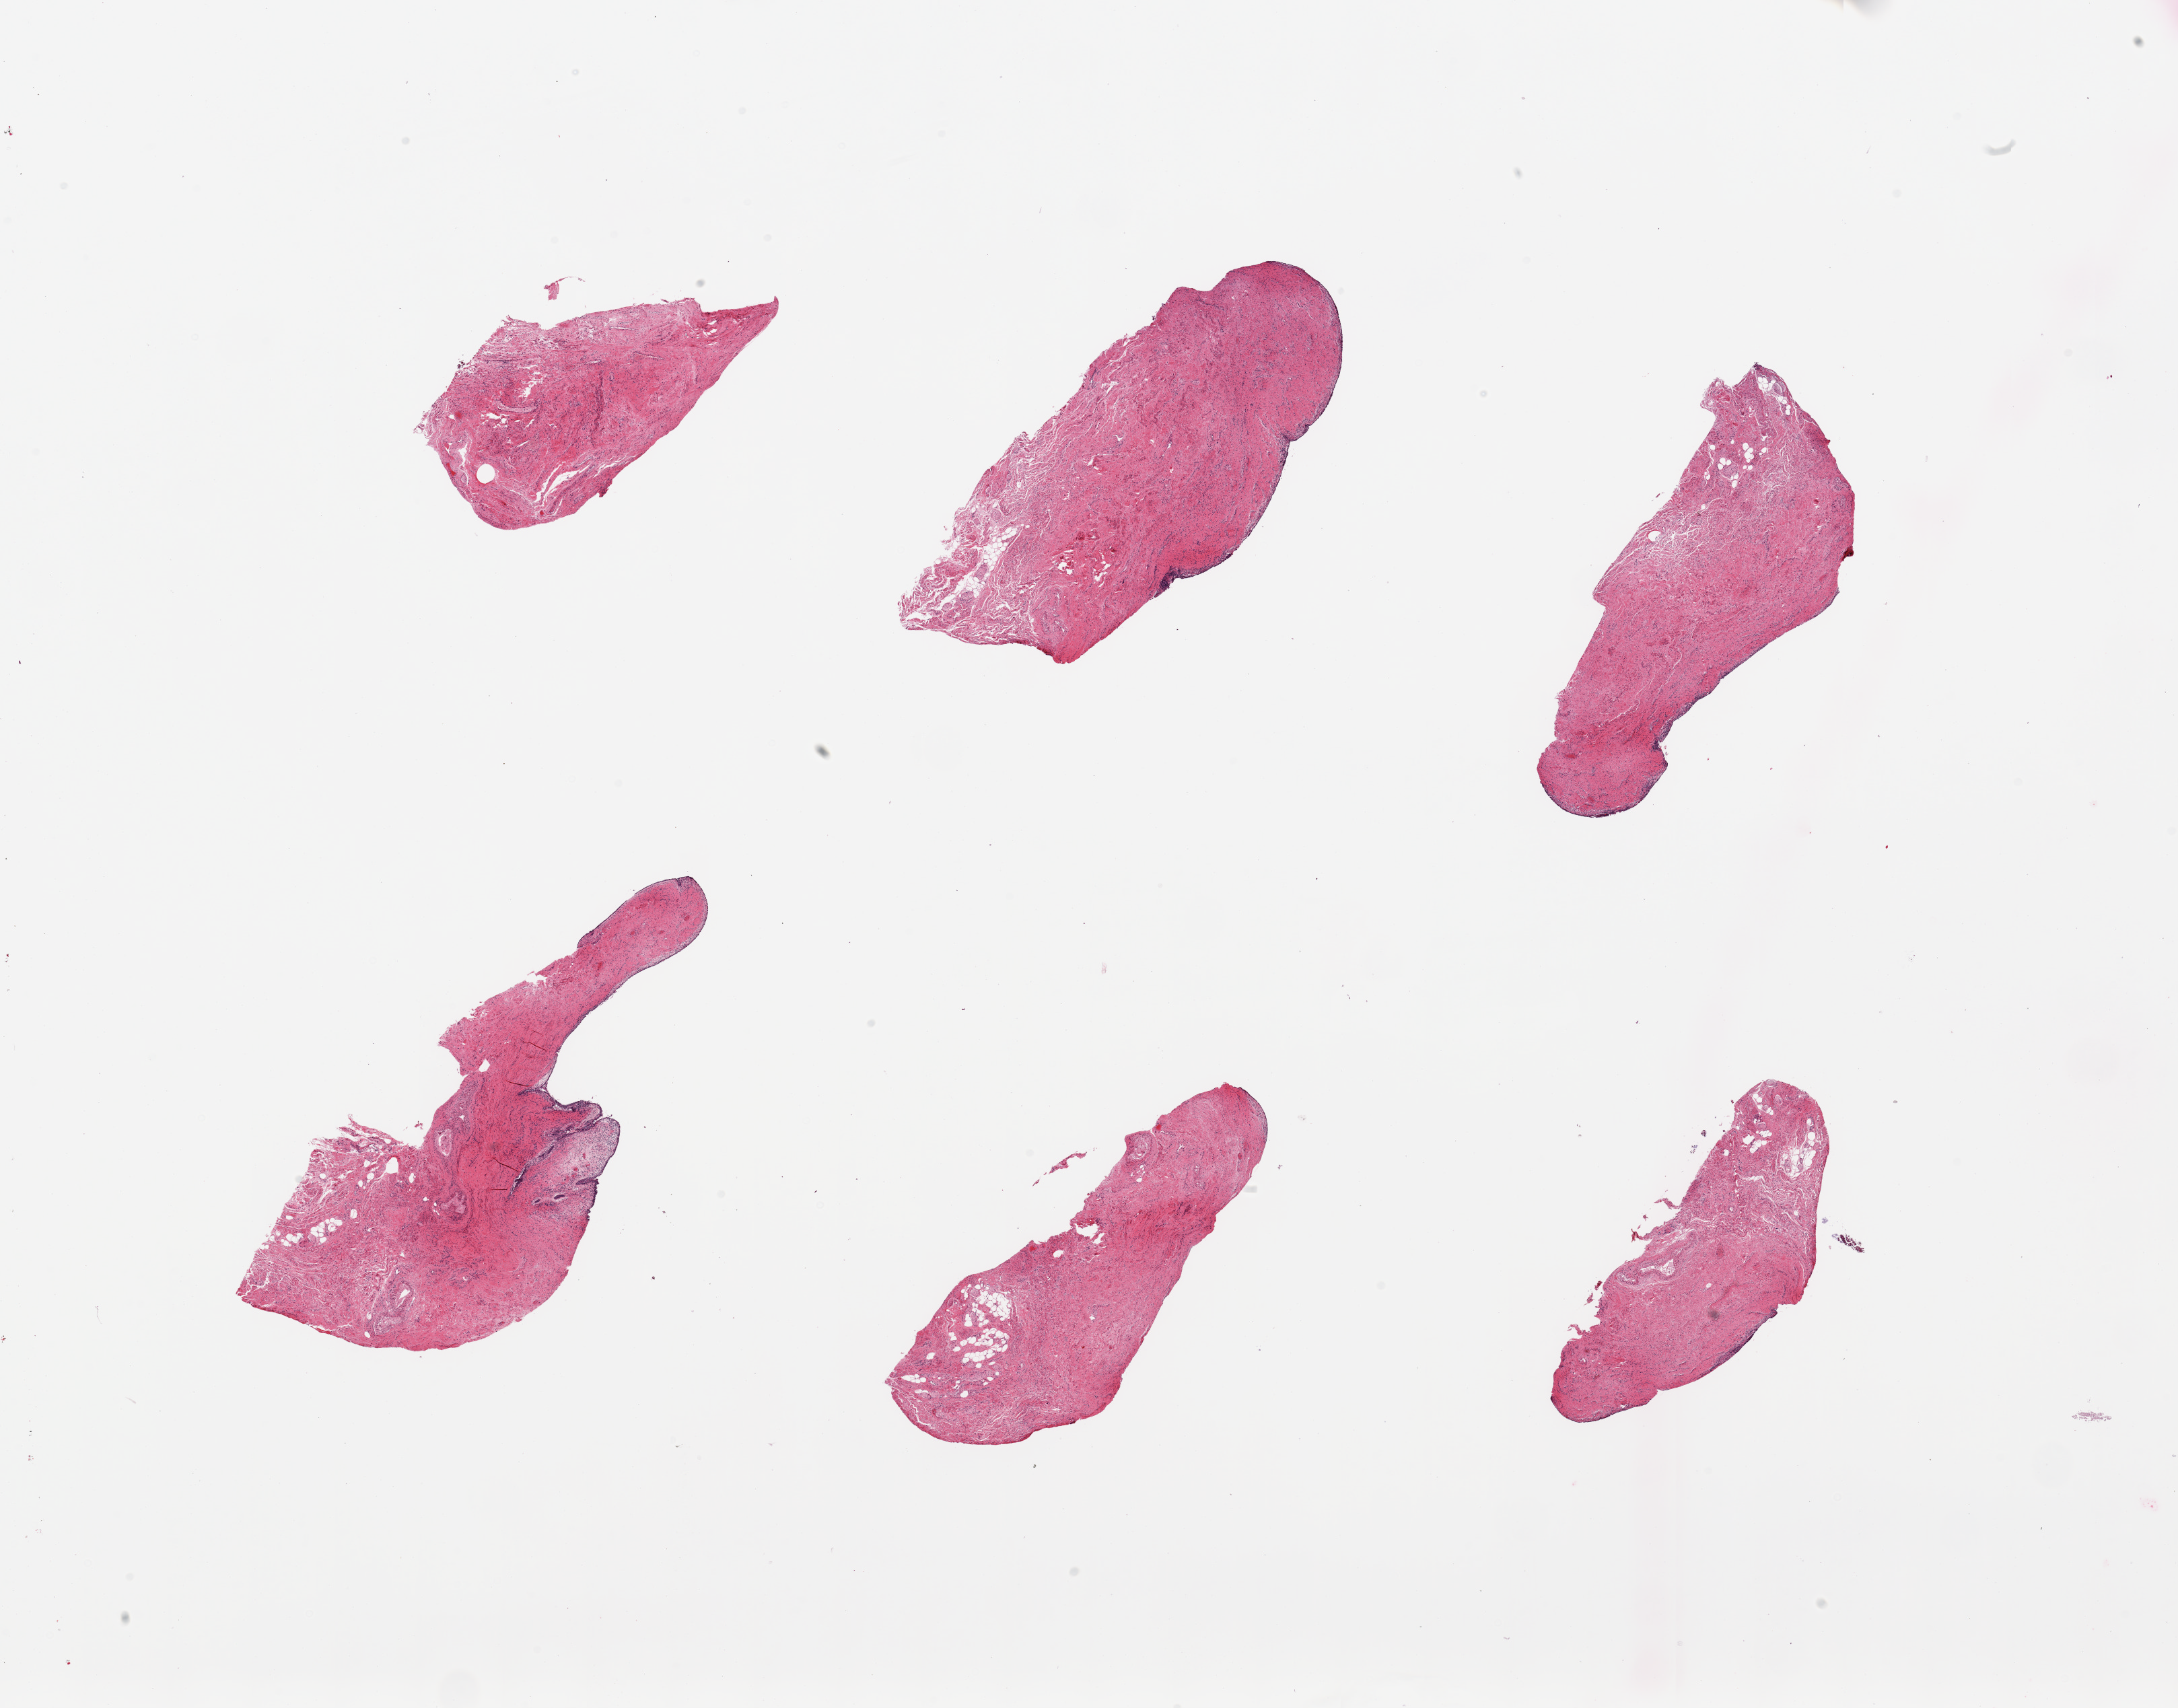
Haematoxylin and eosin whole-slide image, whole scanned area (about 25.6 x 20.1 mm) shown as a low-resolution overview; PAXgene-fixed, paraffin-embedded tissue; section of vagina (target tissue); tissue donor sample.
• pathologist's review note for this sample: 6 pieces; epithelium is atrophic/largely denuded